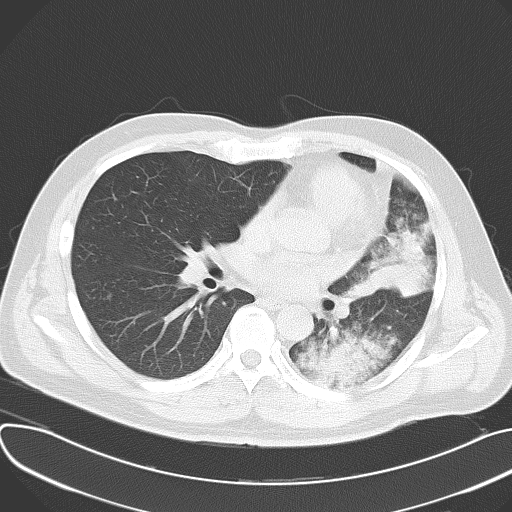
Chest CT, one axial slice; position 33 of 62 along the scan axis; reconstruction kernel B70f; lung window (W 1500 / L -600 HU); 5 mm slice thickness; 512 × 512 image matrix, field of view 377 × 377 mm. Male patient, age 48 years. From the clinical record (not read from this slice): clinical TNM (as recorded): T4 N0 M0.
Outlined on this slice (rectangle marked by the reading radiologist):
- lung tumour (recorded histology: adenocarcinoma): bounding box [x1, y1, x2, y2] px = [339, 219, 438, 306]